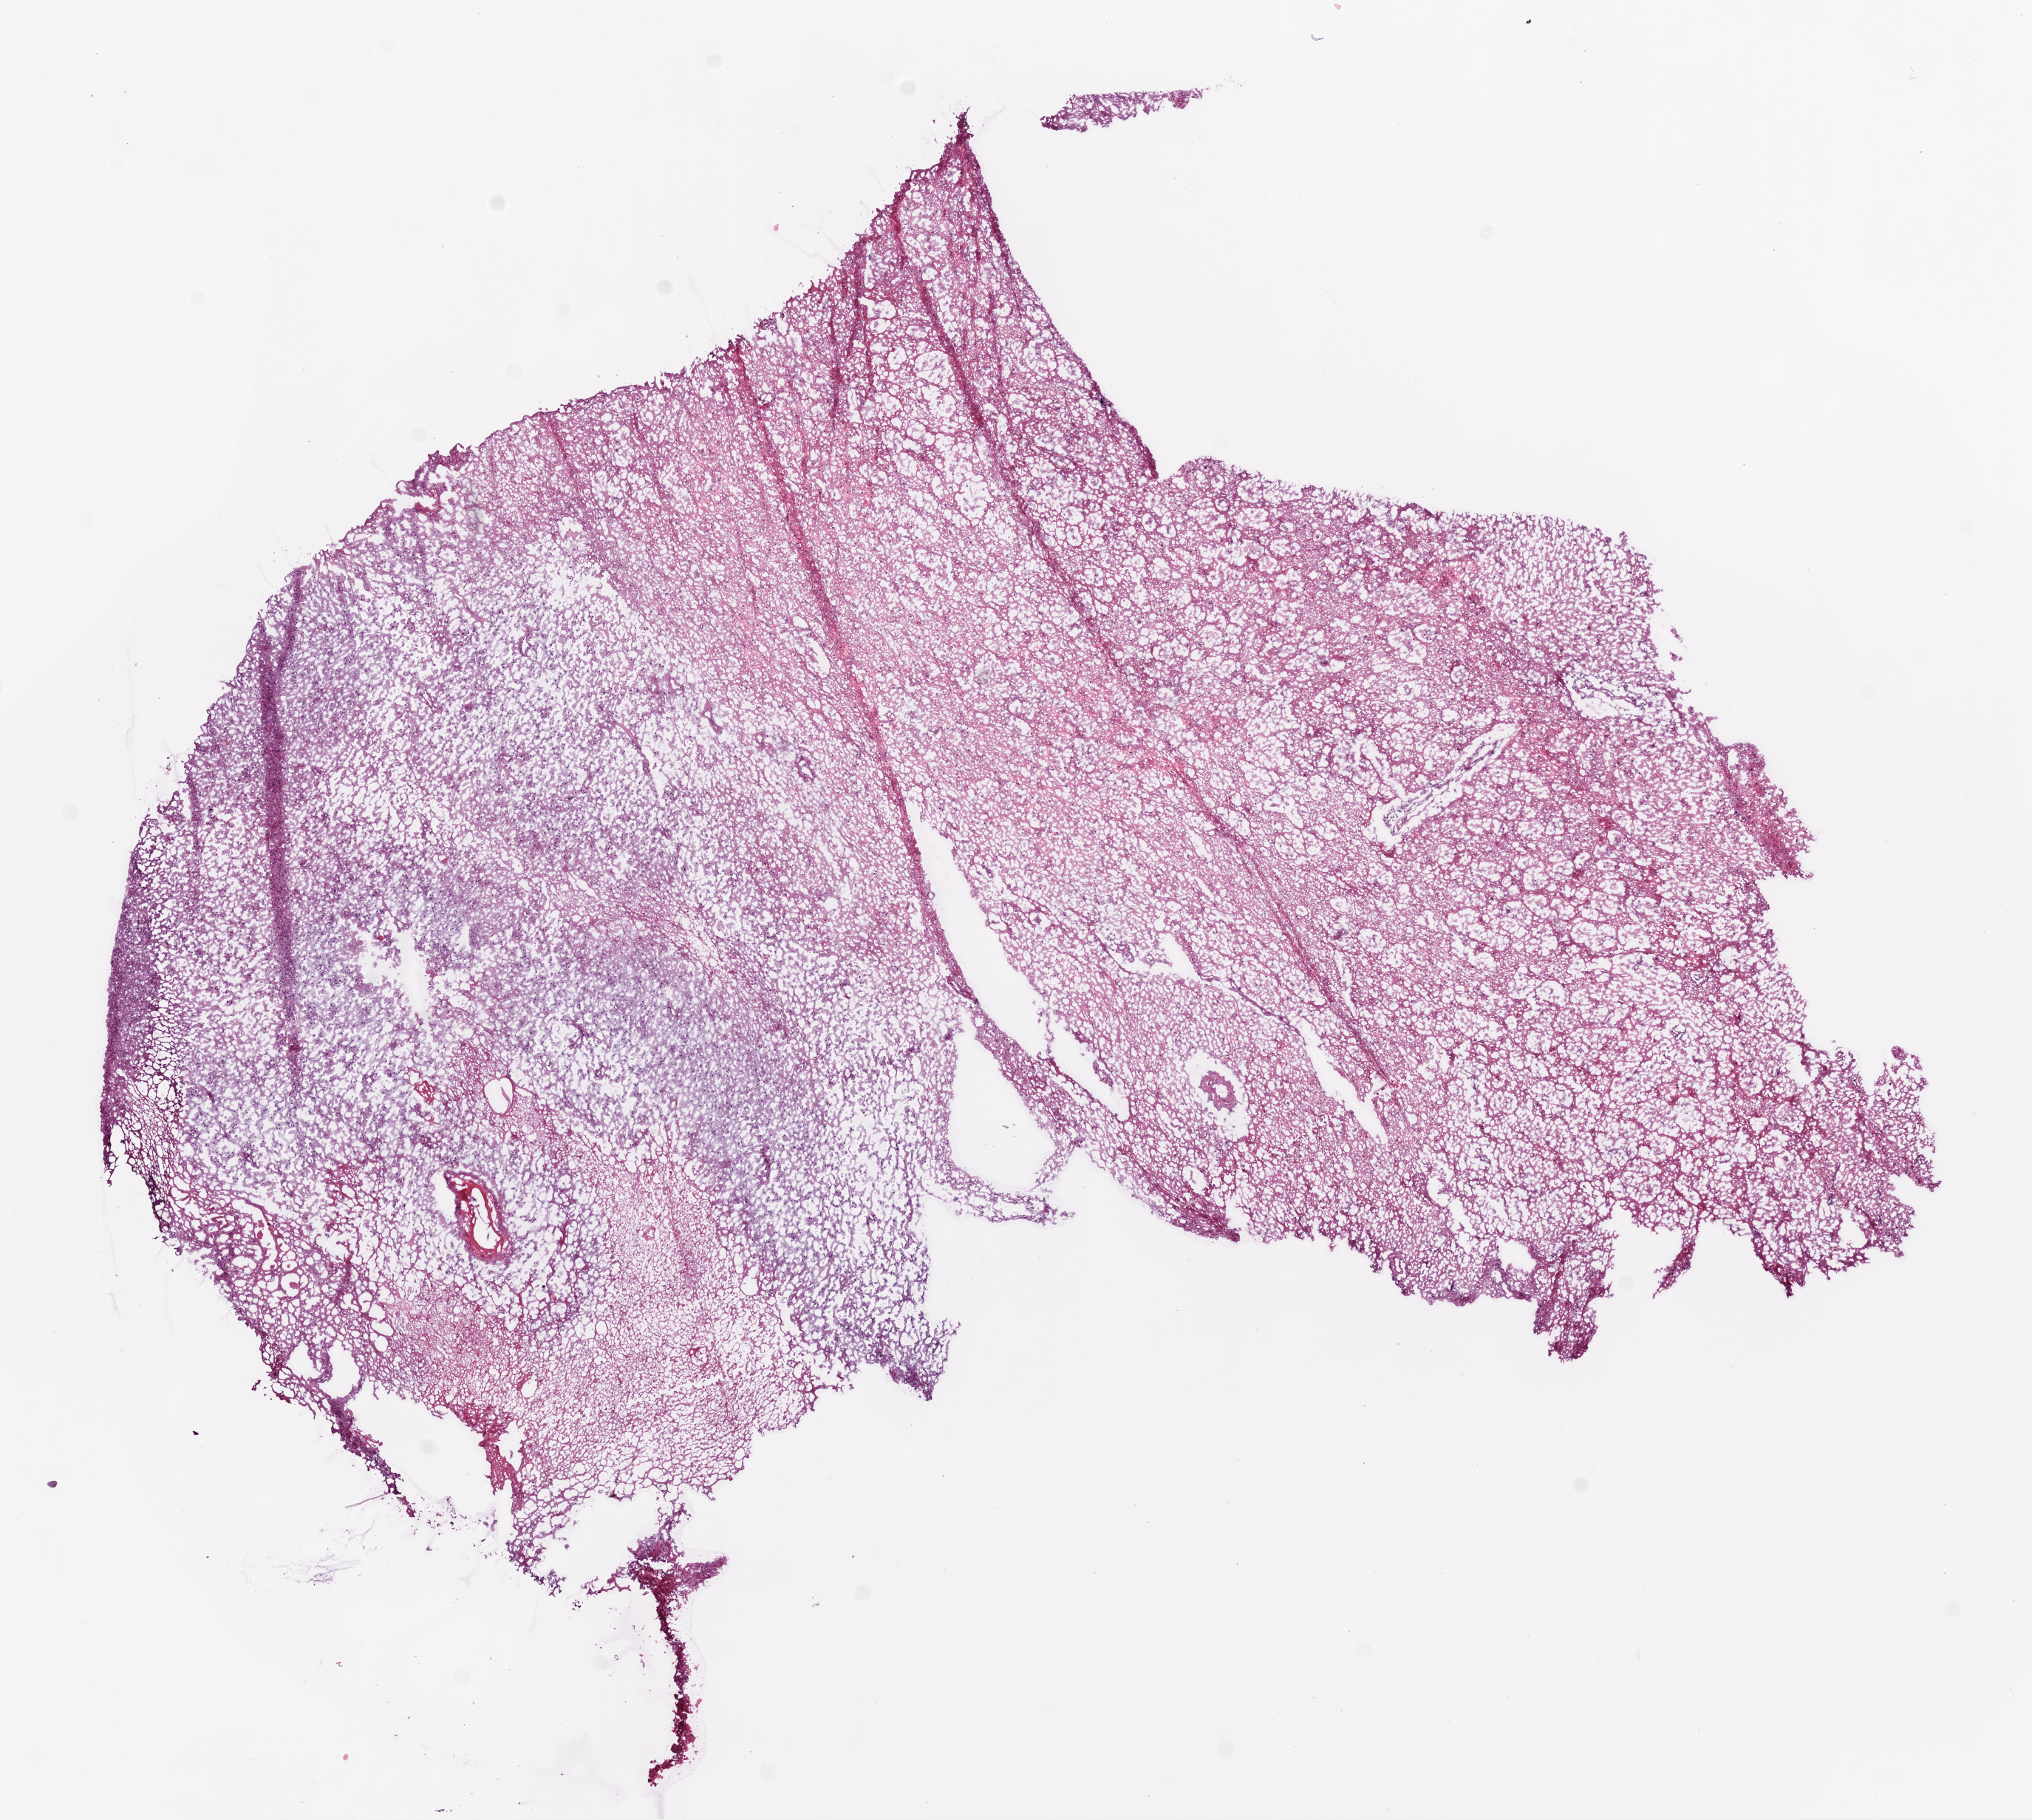
H&E-stained whole-slide image — shown as a low-resolution overview of the whole scanned area (about 11.0 x 9.9 mm, acquisition: 20x scan). Pathologist review of this section (percent, as recorded): tumour cells 95%, tumour nuclei 60%, normal cells 0%, stromal cells 0%, necrosis 5%.
• specimen: frozen section from the bottom of the tissue portion; sample: primary tumour, brain